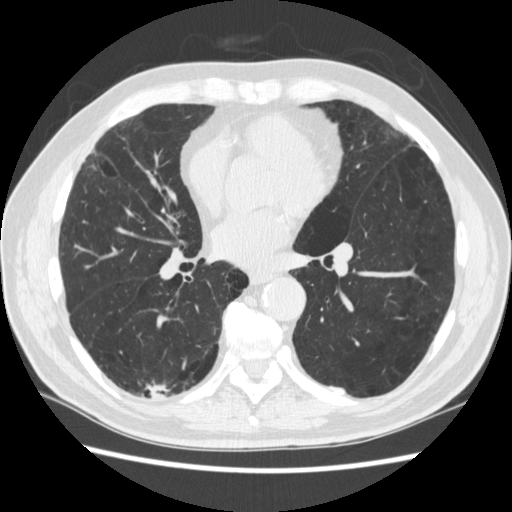
Low-dose screening chest CT, one axial slice; 120 kVp; lung window (W 1500 / L -600 HU); 1.25 mm slice thickness; 512 × 512 image matrix.
Structures marked on this image (expert manual segmentation):
- lesion 1 (tumor, upper lobe of right lung): bounding box (x1, y1, x2, y2) in pixels: (149, 385, 165, 399)